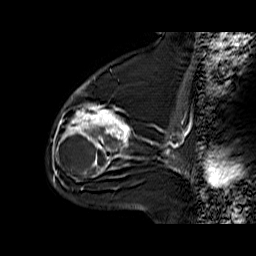
Breast MRI (dynamic contrast-enhanced), one sagittal slice; position 39 of 60 along the scan axis; dynamic contrast-enhanced series, time point 2 of 6 at this slice position (early post-contrast); 1.5 T; TE 6.3 ms, TR 32.9 ms; 4 mm slice thickness; 256 × 256 image matrix. Female patient. Case-level facts recorded for this patient, not image findings: setting: breast cancer imaged before/during neoadjuvant chemotherapy; receptor status: triple-negative.
Outlined on this slice (semi-automatic segmentation, software-assisted and operator-edited):
- analysis volume of interest (the breast-tissue region the enhancement analysis was run in; not a lesion): bounding box [x1, y1, x2, y2] px = [56, 76, 134, 170]
- tumour enhancement mask (voxels above the 100 % enhancement threshold inside the analysis volume of interest): [59, 85, 130, 170]